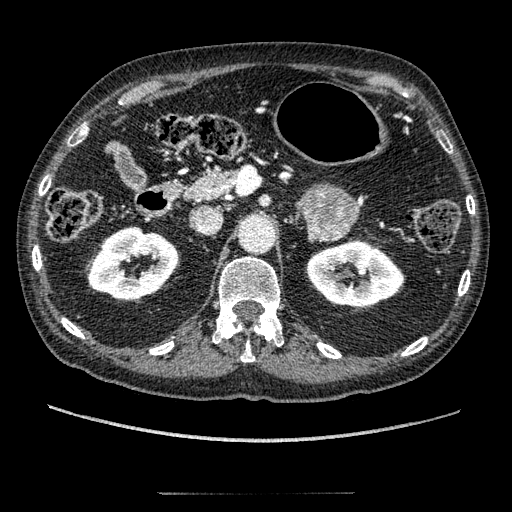
Contrast-enhanced abdominal CT, one axial slice; slice 120 of 274 in the series (ordered by position); reconstruction kernel STANDARD; intravenous contrast given; soft-tissue window (W 400 / L 40 HU); 1.25 mm slice thickness; 512 × 512 image matrix. Patient: male, 69 years. From the clinical record (not read from this slice): diagnosis: adrenocortical carcinoma; tumour side: left adrenal; tumour size at pathology: 6.1 cm; Ki-67 index: 10 %; stage (as recorded): 3.
Structures marked on this image (semi-automatic segmentation, software-assisted and operator-edited):
- mass: bounding box <297,186,358,241> (left, top, right, bottom; pixels)